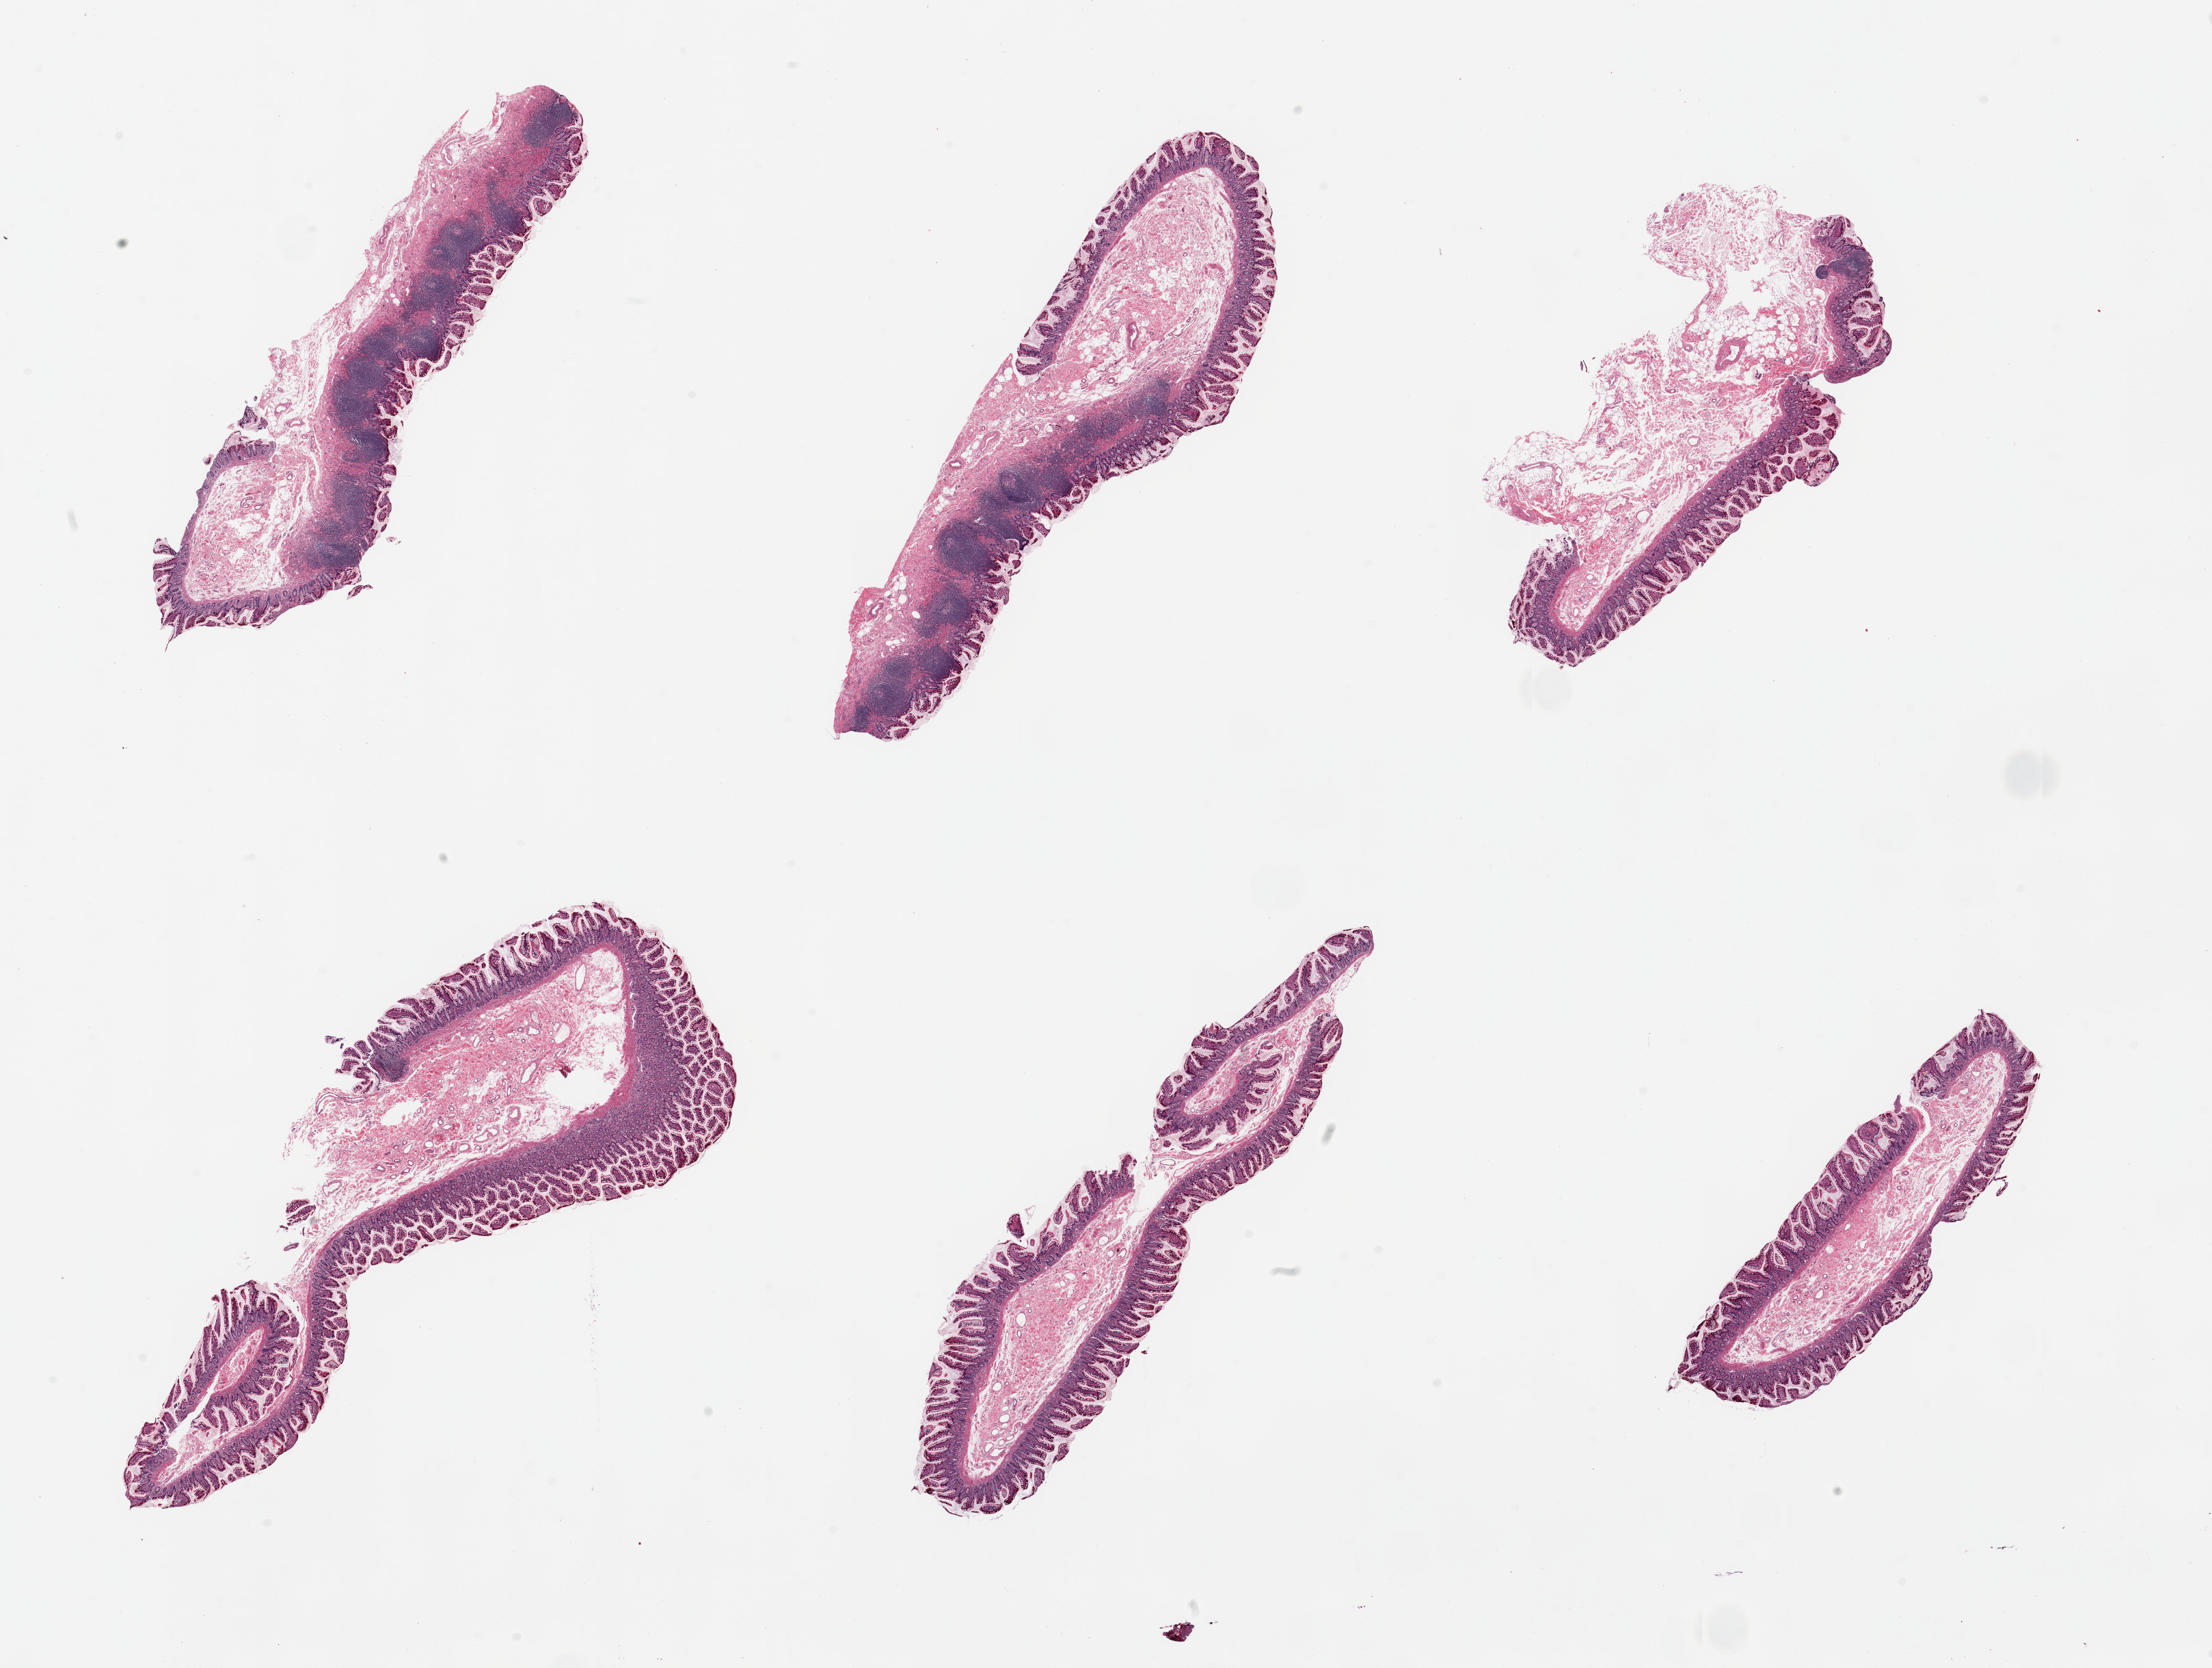
Digitized H&E-stained section, brightfield, whole scanned area (about 25.6 x 19.3 mm) shown as a low-resolution overview; PAXgene-fixed, paraffin-embedded tissue; sampled site (target tissue): ileum; donor tissue sample. Donor: male.
Review note (as recorded): 6 pieces, well preserved; lymphoid aggregates, ~20% tissue.